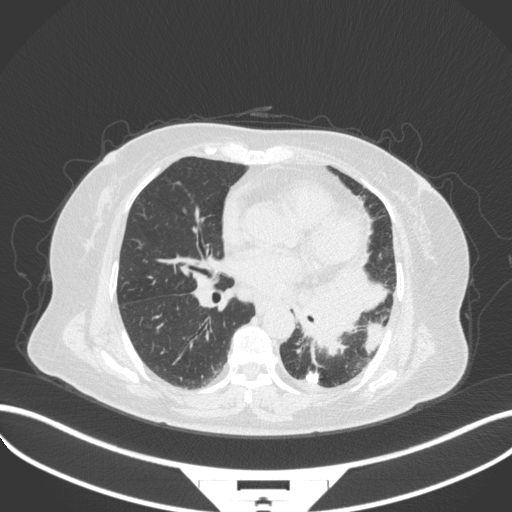
Chest CT, one axial slice. Position 166 of 328 along the scan axis. Reconstruction kernel B31f. Lung window (W 1500 / L -600 HU). 1 mm slice thickness. 512 × 512 image matrix, field of view 400 × 400 mm. Patient: female, 69 years. From the clinical record (not read from this slice): clinical TNM (as recorded): T2b N3 M1.
Annotated regions visible in this slice (rectangle marked by the reading radiologist):
- lung tumour (recorded histology: adenocarcinoma): bounding box <290,264,388,356> (left, top, right, bottom; pixels)